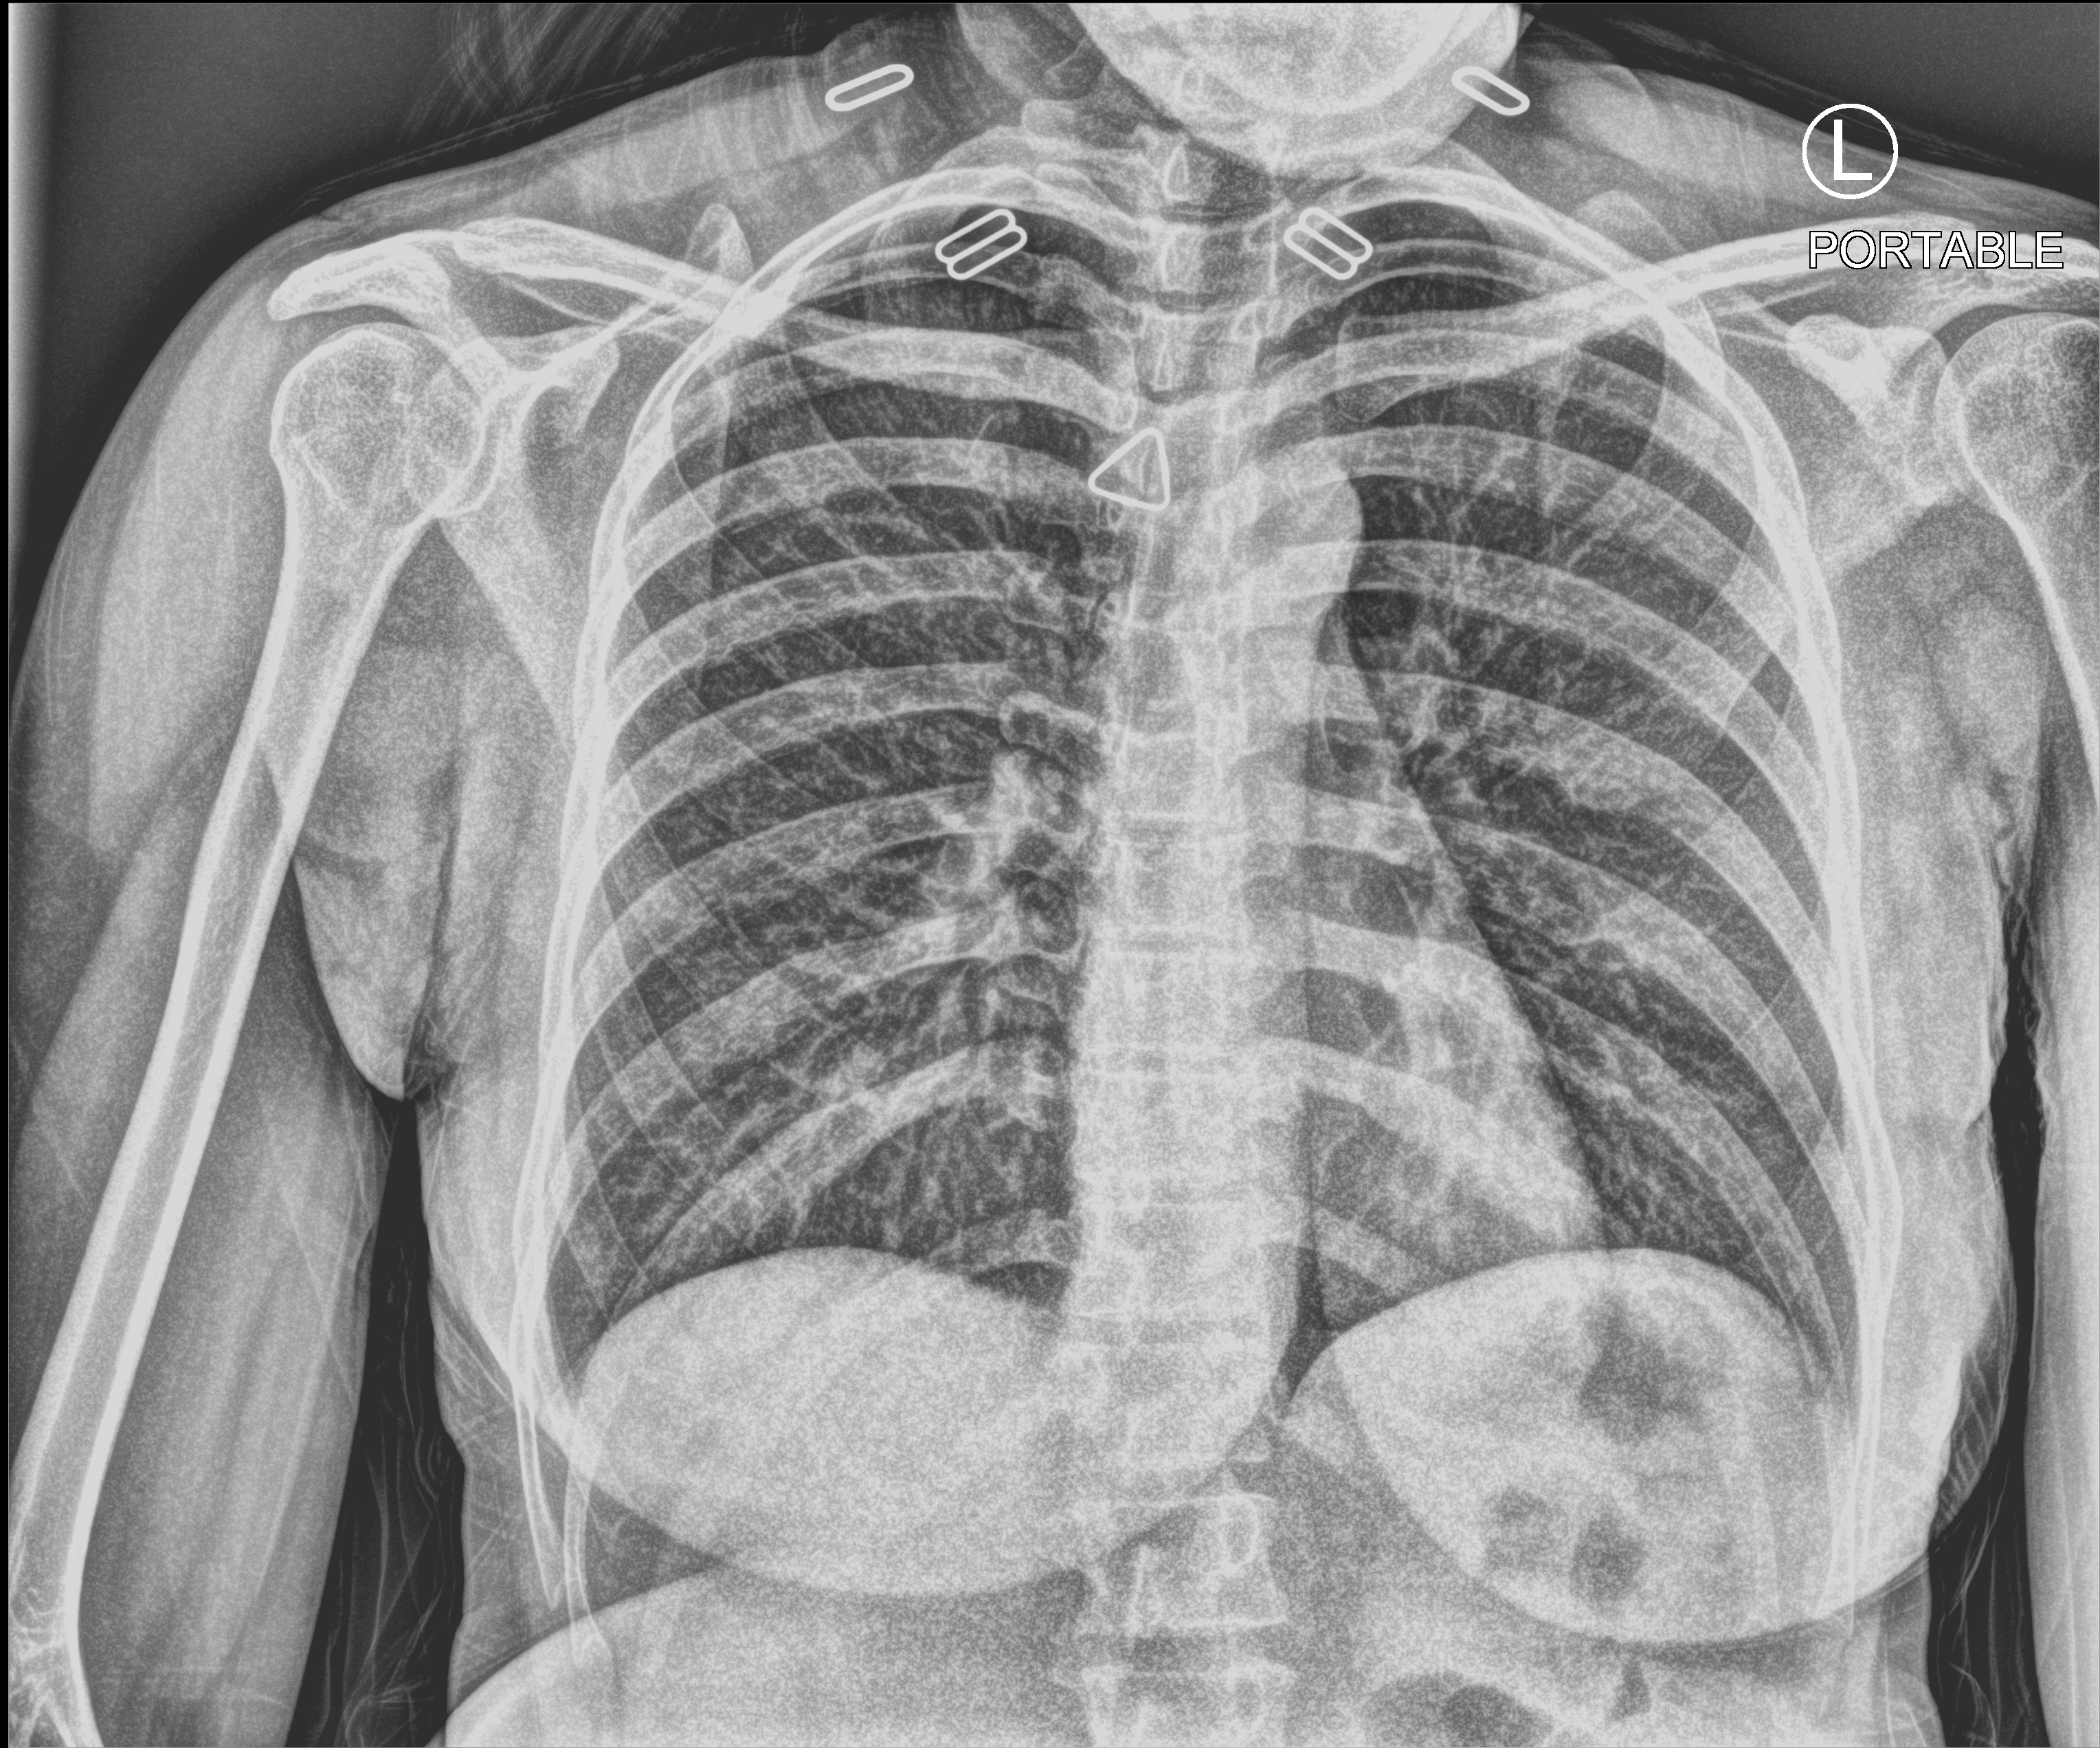
Bedside chest radiograph (computed radiography). Female patient hospitalised with COVID-19, age 18–59 years.
Hospital-stay facts (about this admission, not read from this image; timing relative to this image not recorded): admitted to intensive care during this hospital stay: no; mechanically ventilated during this hospital stay: no.